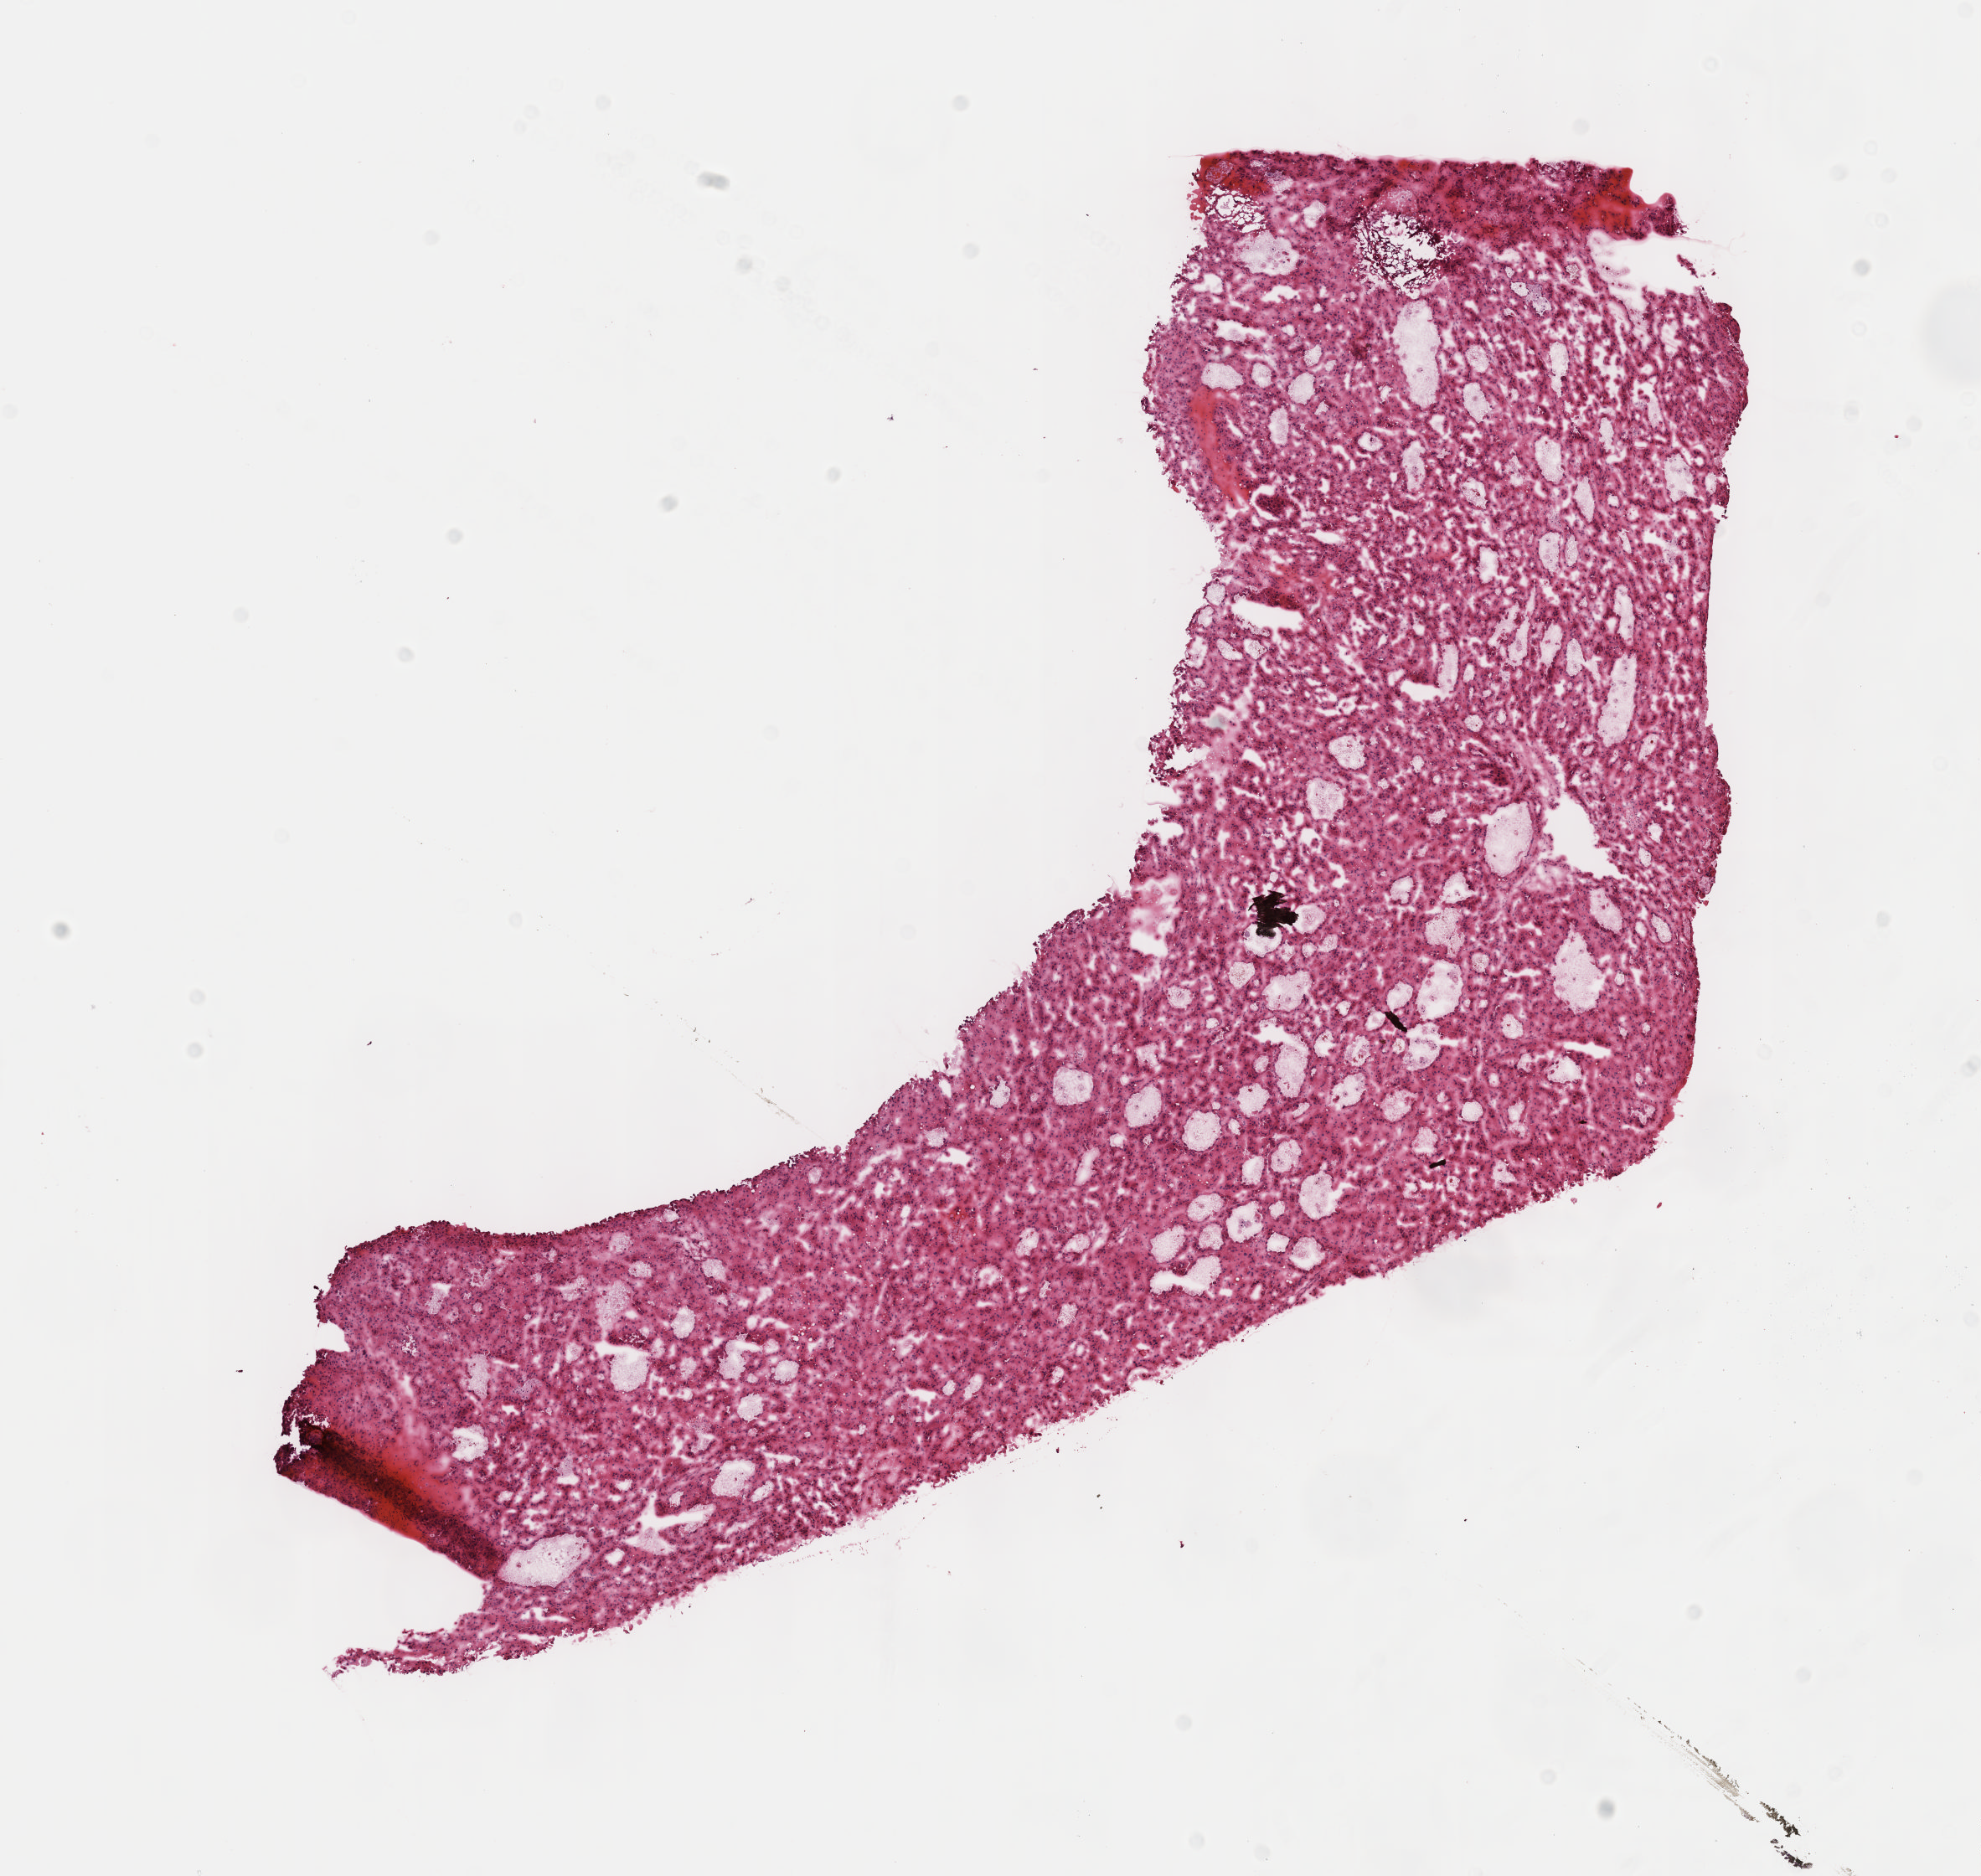
H&E whole-slide image — whole scanned area (about 9.6 x 9.1 mm, acquisition: 40x scan) shown as a low-resolution overview; frozen section from the top of the tissue portion; primary tumour sample from the liver. Patient: male, age at initial diagnosis 50 years. Composition of this section per pathologist review: tumour cells 100%, tumour nuclei 80%.
Histologic diagnosis: Hepatocellular carcinoma, NOS.